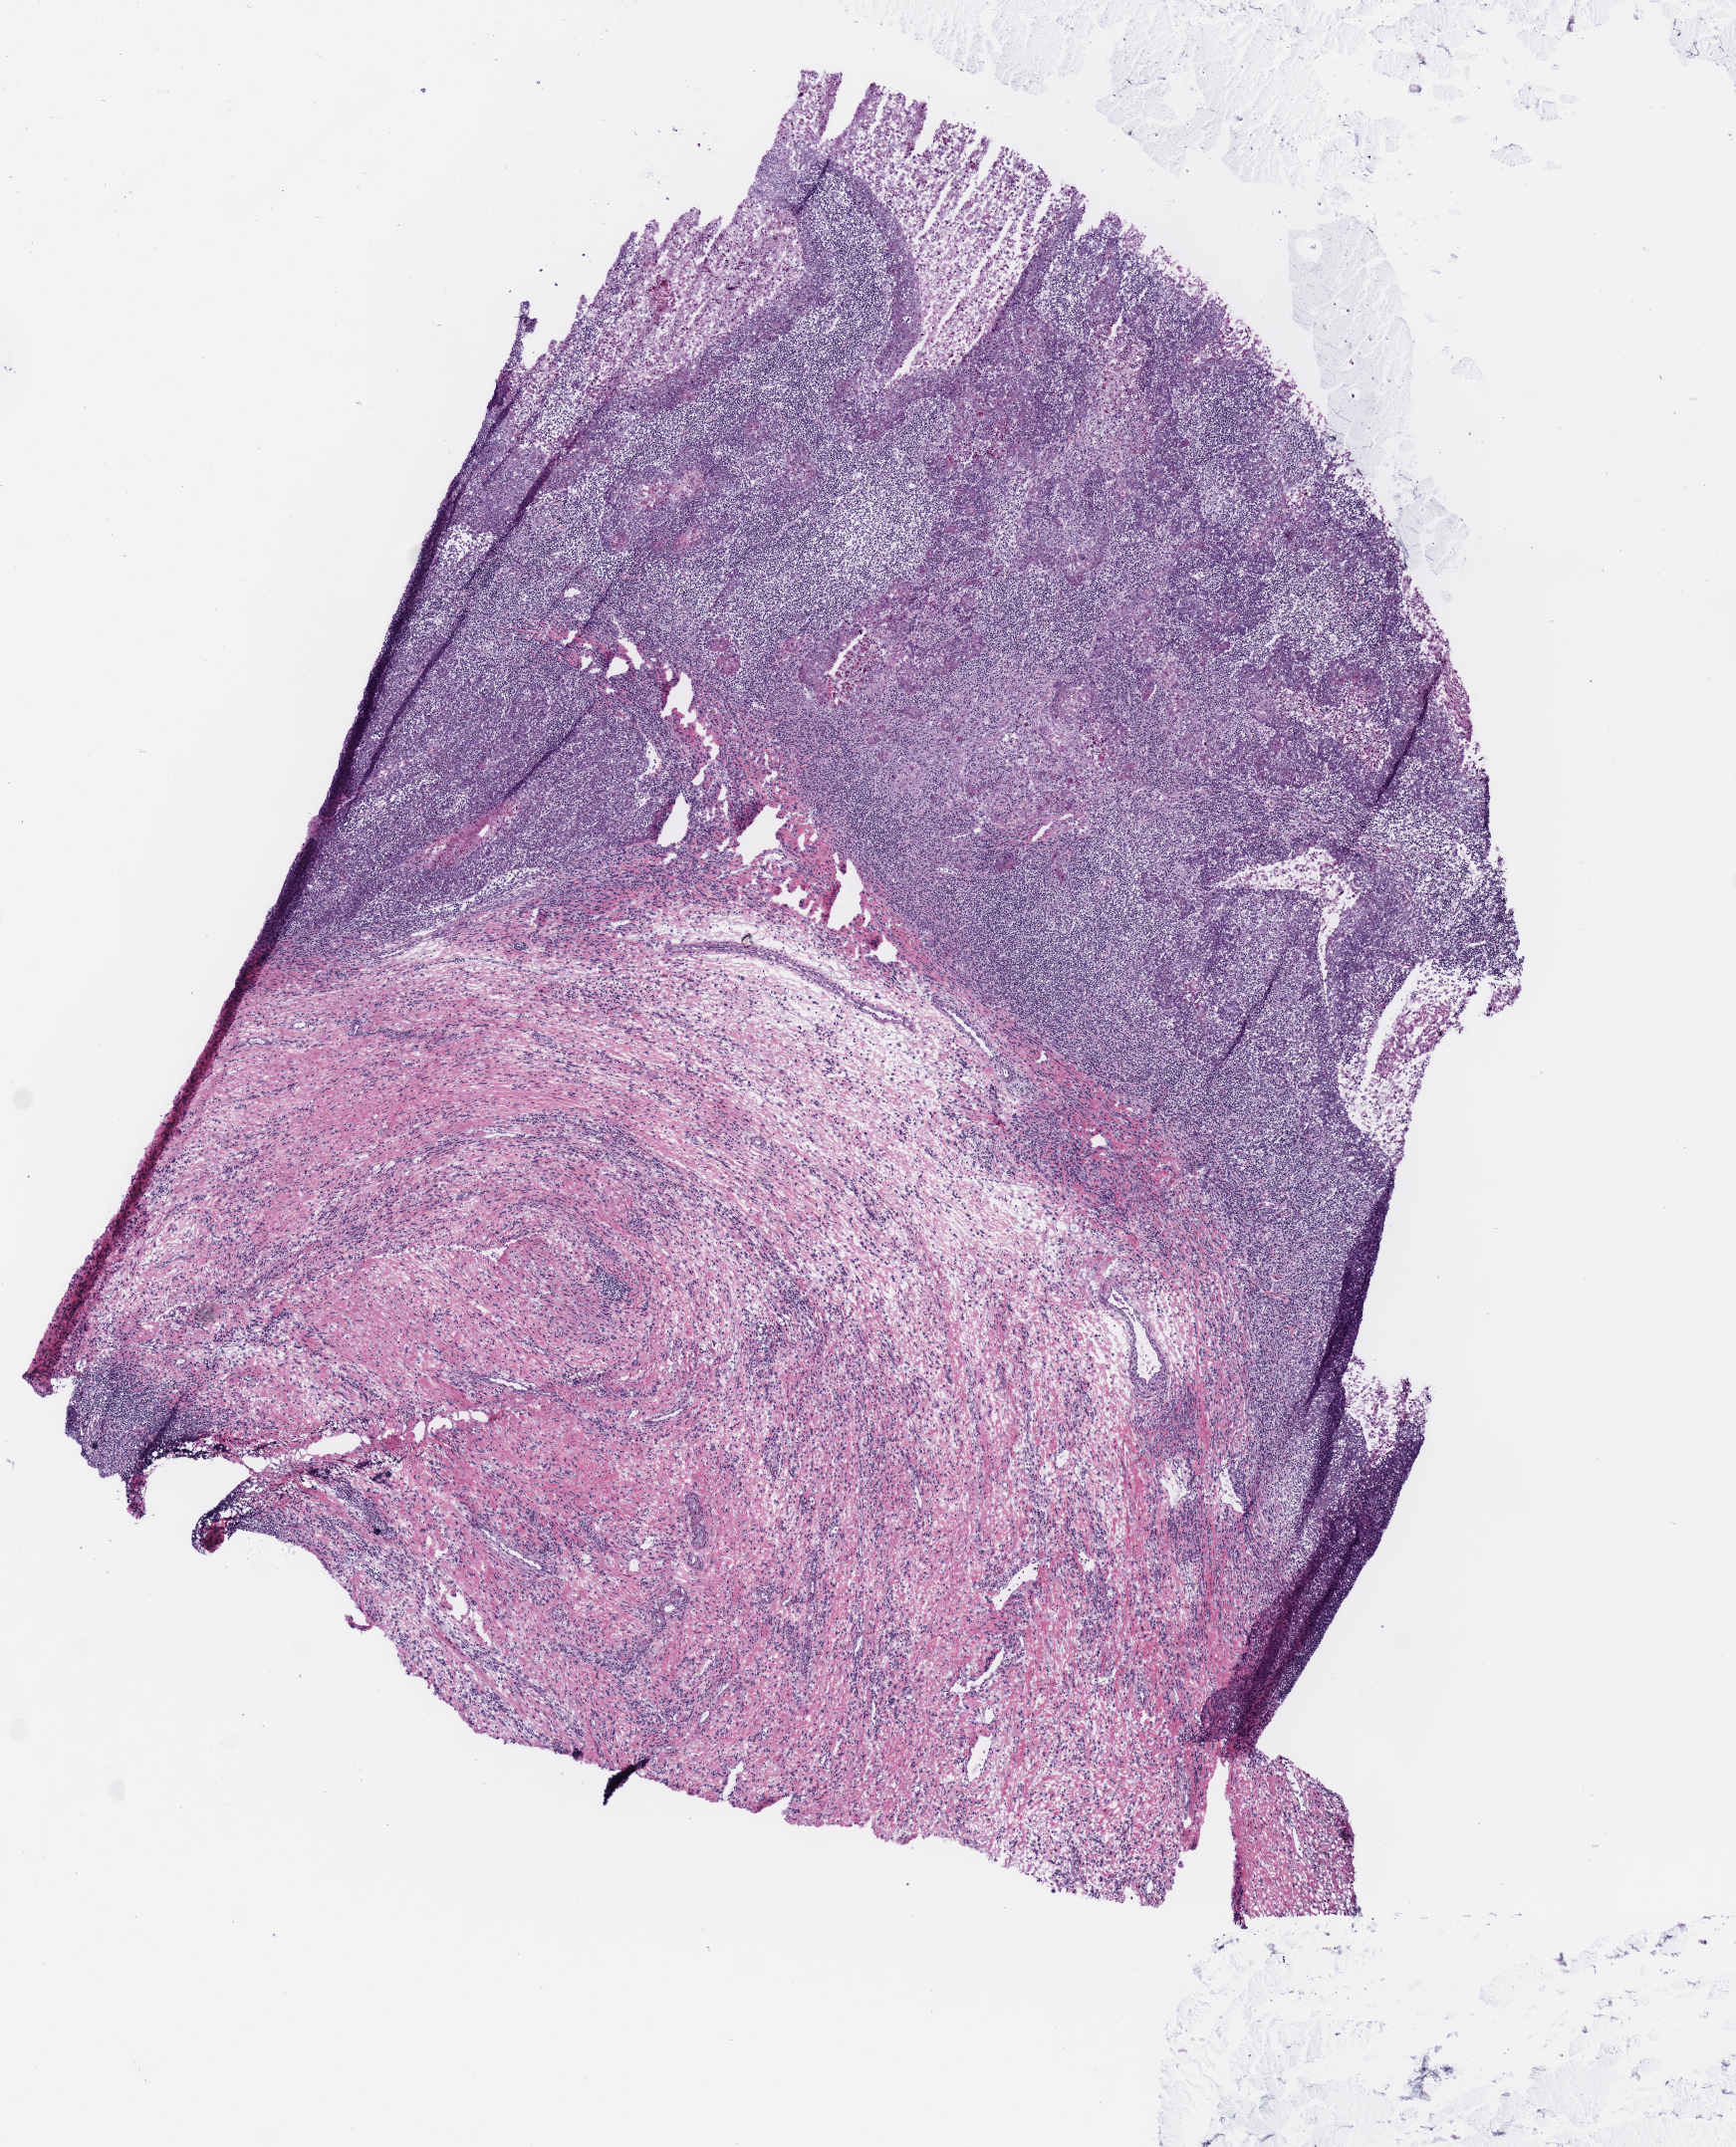
H&E whole-slide image — low-resolution overview of the scanned area, about 6.9 x 8.5 mm. Frozen section. Primary tumour sample from the head and neck. Male patient; age at initial diagnosis 56 years. Pathologist review of this section (percent, as recorded): tumour cells 50%, tumour nuclei 15%, normal cells 0%, stromal cells 40%, necrosis 10%.
- diagnosis: Squamous cell carcinoma, NOS (base of tongue, NOS)
- AJCC pathologic stage: III (7th edition)